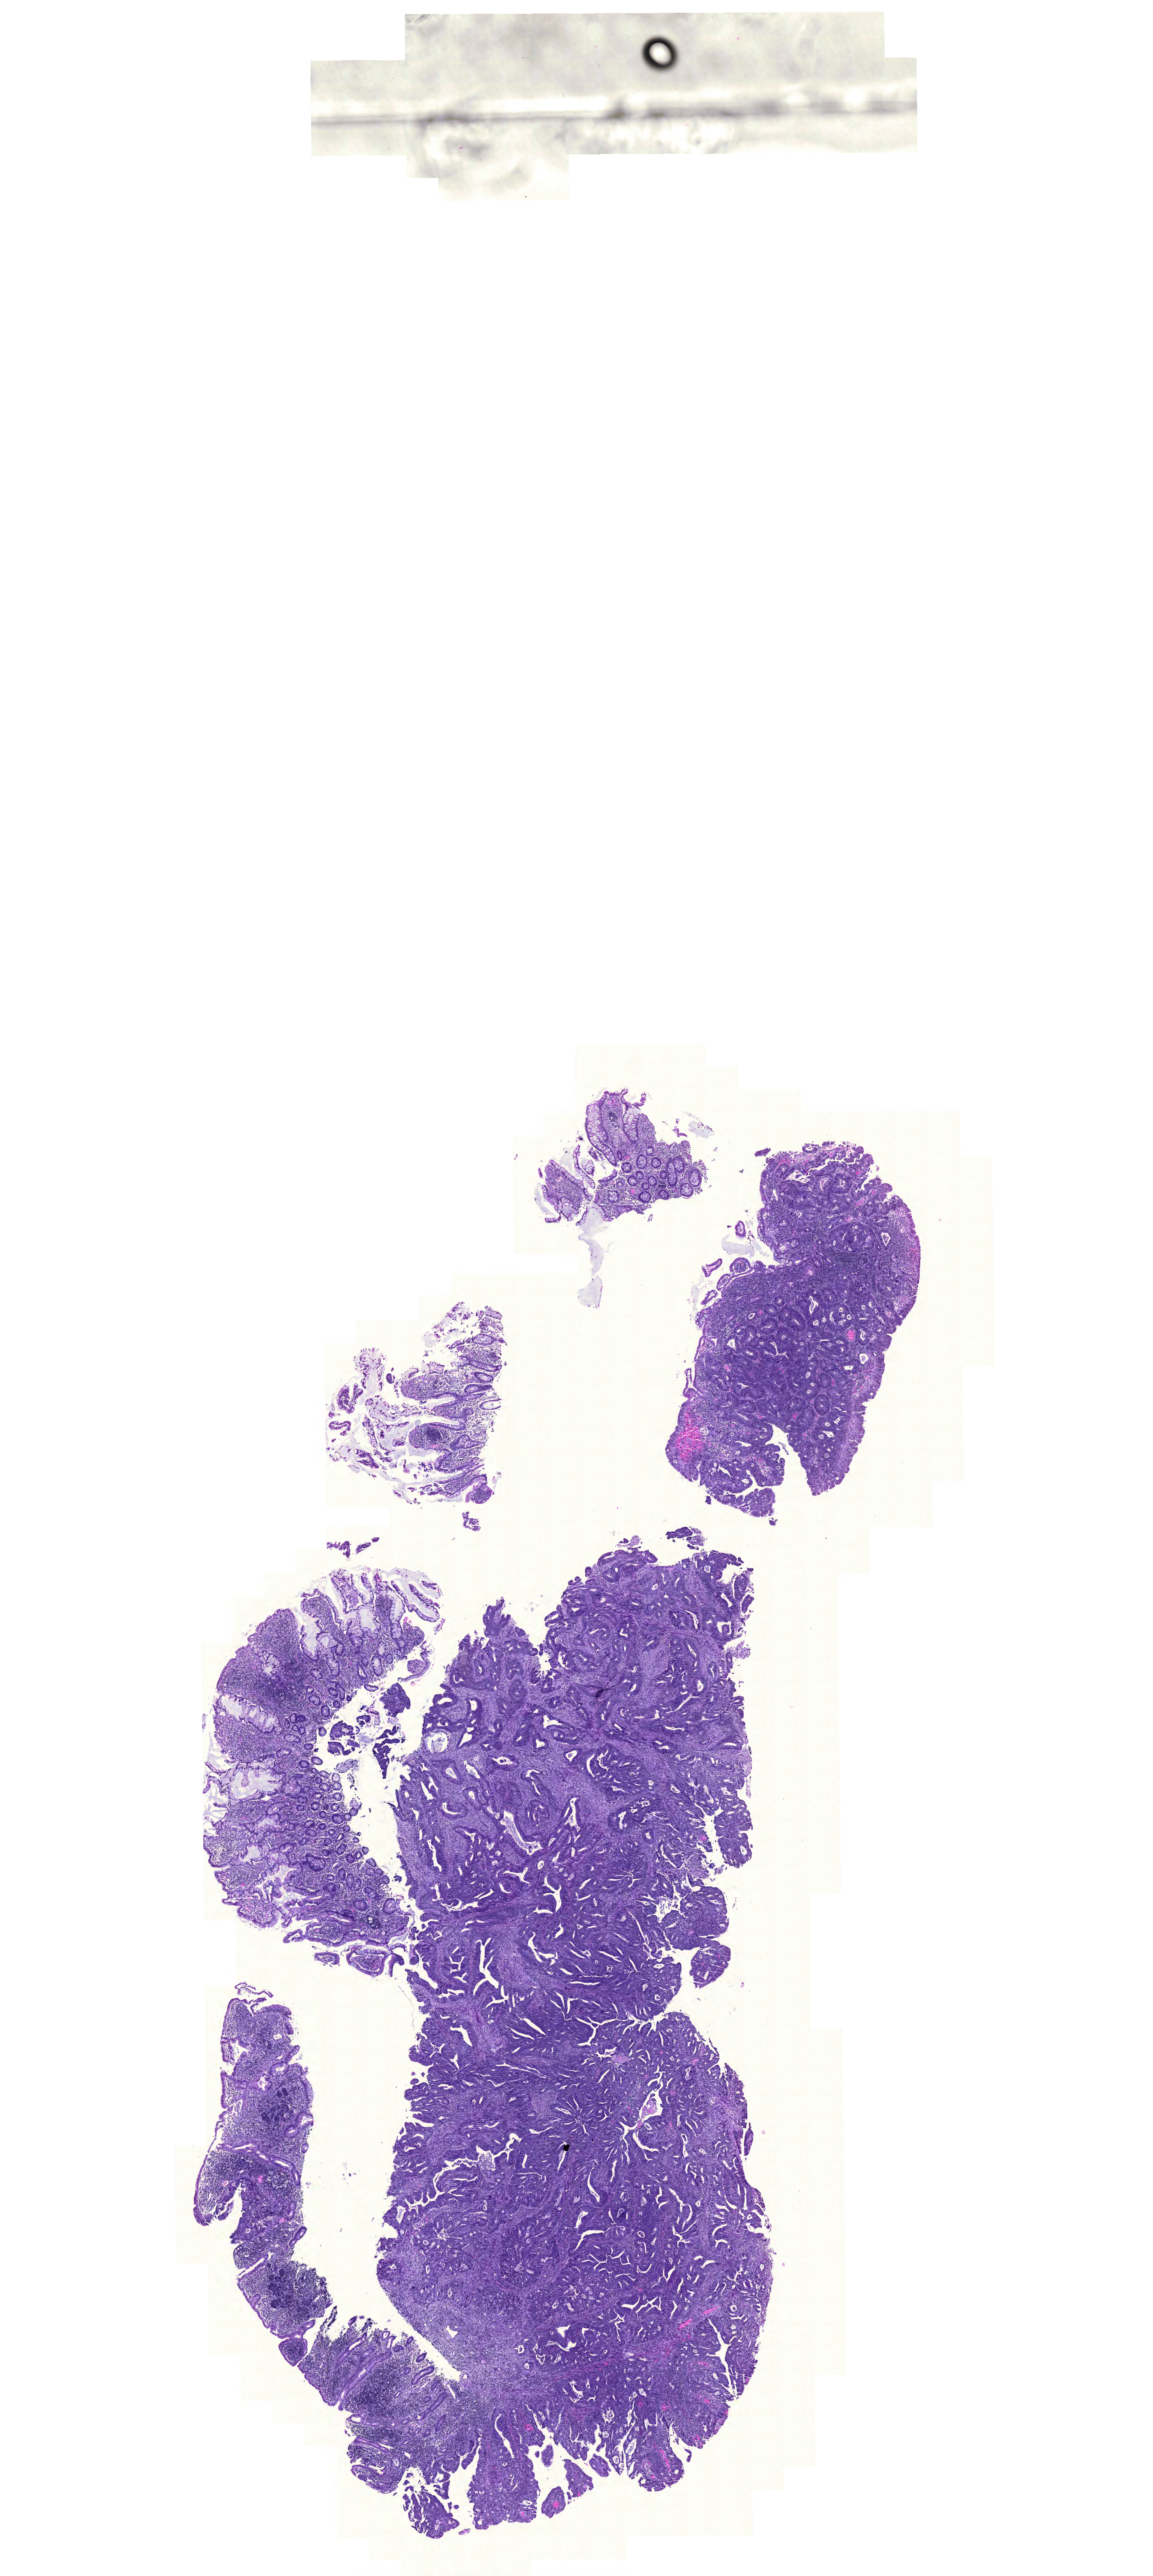
H&E whole-slide image — shown as a low-resolution overview of the whole scanned area (about 10.4 x 23.3 mm), formalin-fixed paraffin-embedded (FFPE) diagnostic section, primary tumour sample from the colon. Female patient; age at initial diagnosis 71 years.
- lymph nodes positive (case pathology): 4 of 23 examined
- histologic diagnosis: Adenocarcinoma, NOS
- AJCC pathologic stage: IIIC (6th edition)